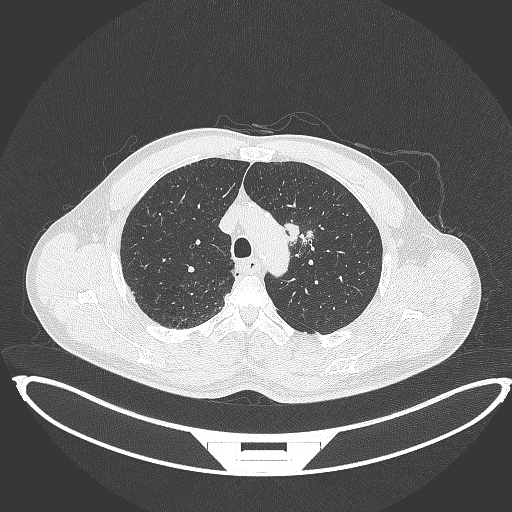
Chest CT, one axial slice; slice 331 of 395 in the series (ordered by position); reconstruction kernel B70f; lung window (W 1500 / L -600 HU); 512 × 512 image matrix, field of view 457 × 457 mm. Patient: male, 60 years. Case-level facts recorded for this patient, not image findings: clinical TNM (as recorded): T2a N0 M0.
Structures marked on this image (bounding box drawn by a radiologist):
- lung tumour (recorded histology: squamous cell carcinoma): bounding box <282,218,315,248> (left, top, right, bottom; pixels)